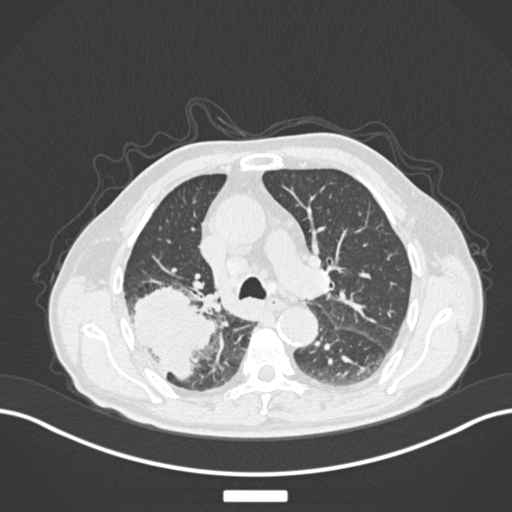
Chest CT, one axial slice. Position 118 of 201 along the scan axis. Lung window (W 1500 / L -600 HU). 512 × 512 image matrix, field of view 400 × 400 mm. Patient: male, 72 years. Case-level facts recorded for this patient, not image findings: clinical TNM (as recorded): T3 N2 M0.
Annotated regions visible in this slice (bounding box drawn by a radiologist):
- lung tumour (recorded histology: adenocarcinoma): box from (x=132, y=283) to (x=217, y=384) px